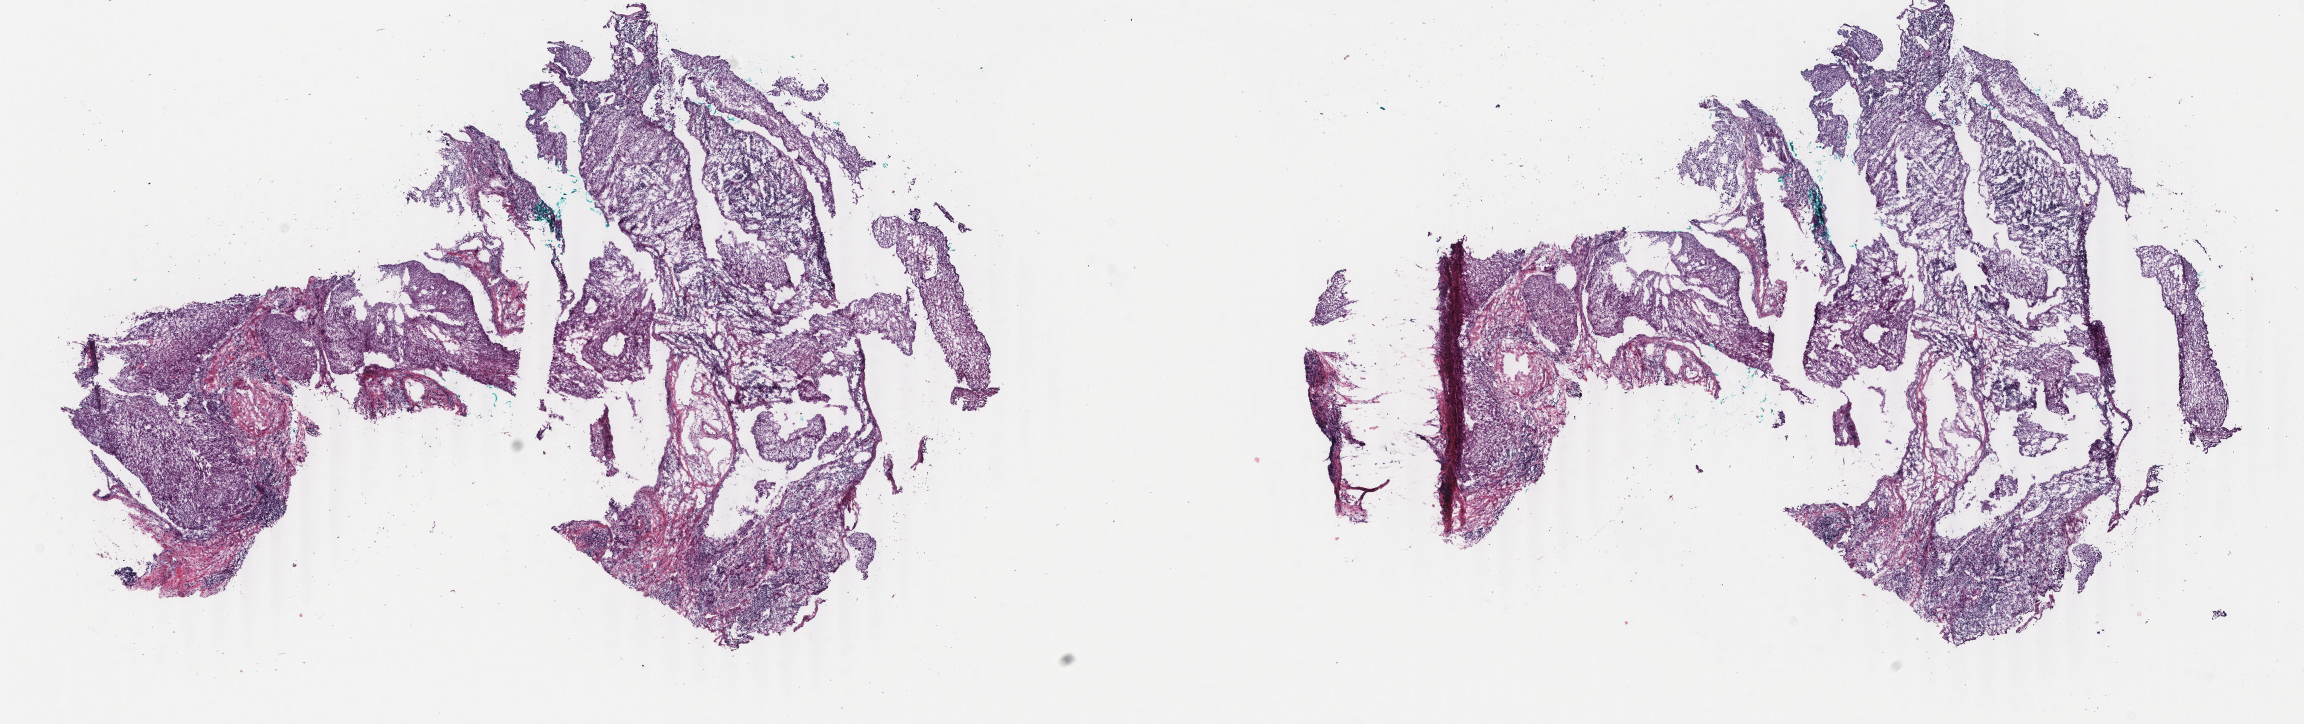
Whole-slide histology image, Hematoxylin and eosin (H&E) stained, whole scanned area (about 18.3 x 5.8 mm) shown as a low-resolution overview. Frozen section. Primary tumour sample from the cervix. Female, age 61 years at initial diagnosis. Histologic grade: G2 (moderately differentiated). Composition of this section per pathologist review: tumour cells 50%, tumour nuclei 50%, normal cells 0%, stromal cells 50%, necrosis 0%. Inflammatory infiltration, as recorded: lymphocyte infiltration 20%, monocyte infiltration 0%, neutrophil infiltration 3%.
FIGO stage: IIIB. Pathologic diagnosis: Squamous cell carcinoma, NOS (cervix uteri).